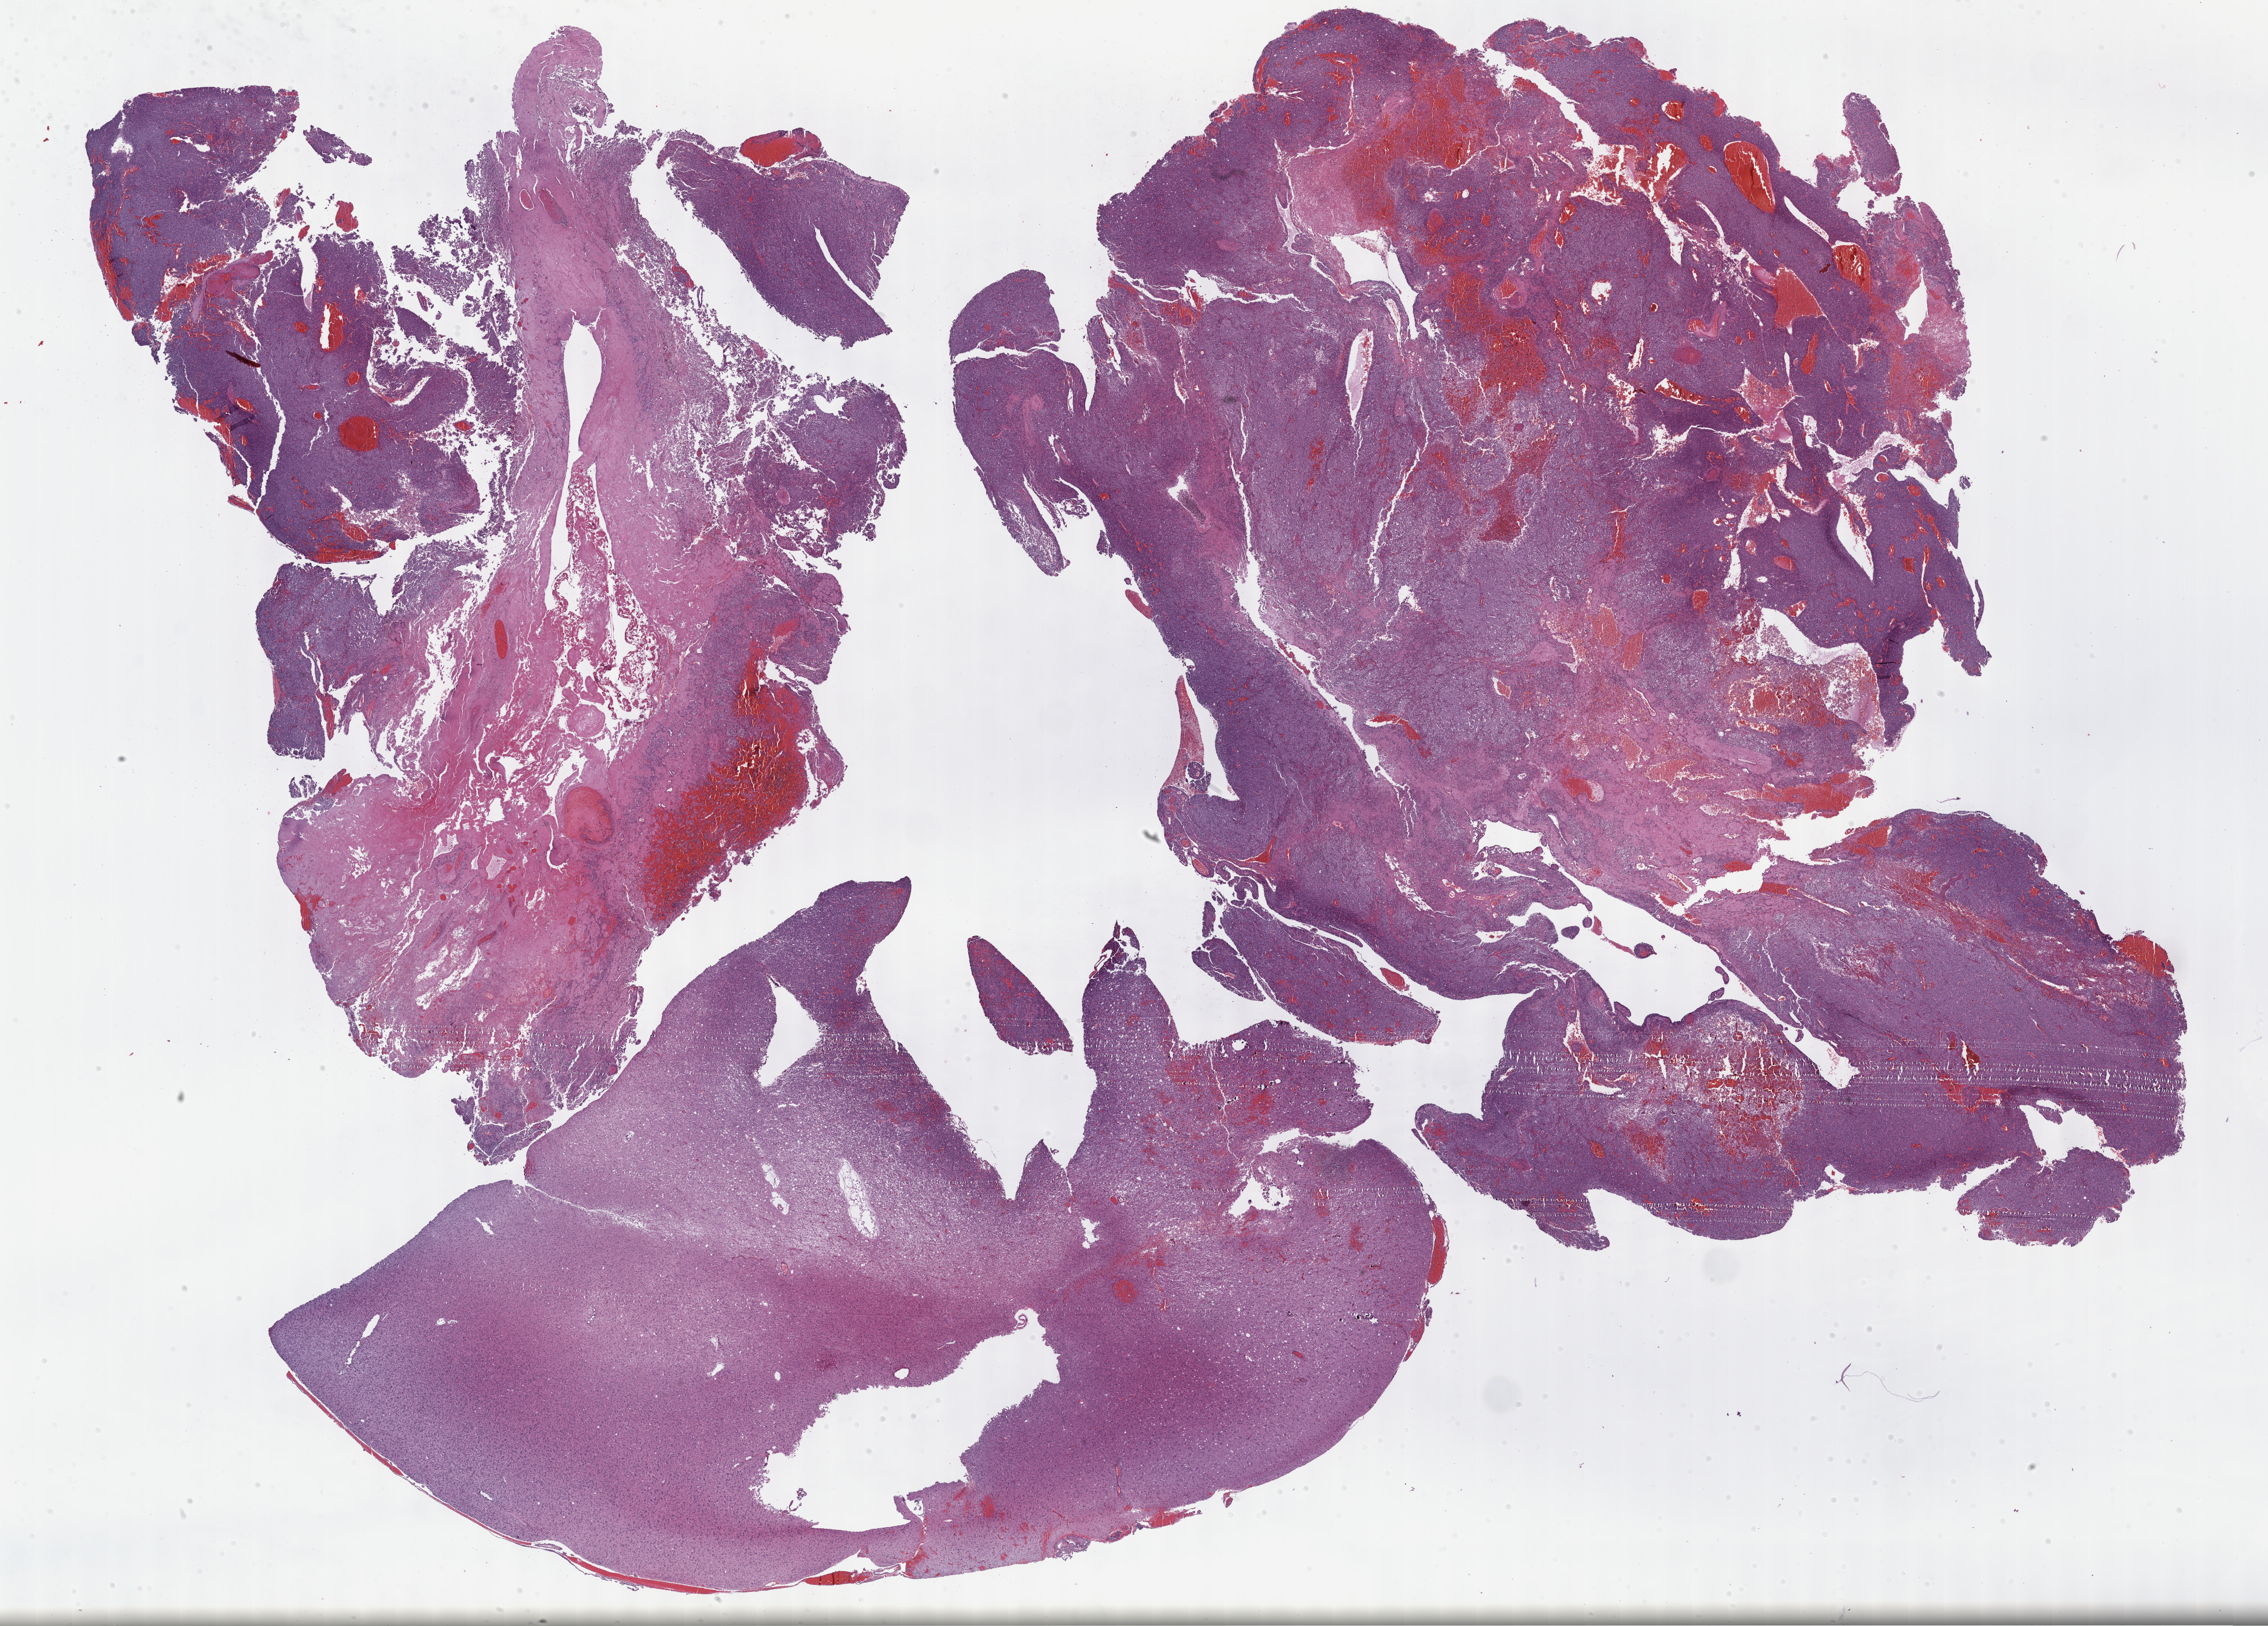
H&E whole-slide image — whole scanned area (about 31.7 x 22.7 mm) shown as a low-resolution overview. Formalin-fixed paraffin-embedded (FFPE) diagnostic section. Brain, primary tumour sample. Male patient; age at initial diagnosis 33 years. Histologic grade: G3 (poorly differentiated).
Pathologic diagnosis: Oligodendroglioma, anaplastic (cerebrum).